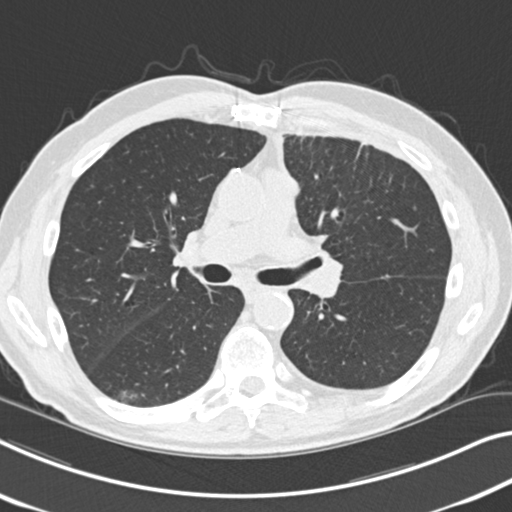
Axial slice from a low-dose chest CT screening exam, first (baseline) screen, lung window (W 1500 / L -600 HU), 2 mm slice thickness, 512 × 512 image matrix, field of view 338 × 338 mm. Male, age 68 years at enrolment. Current smoker at enrolment.
Expert reader's lesion annotation, bounding box <99,379,150,413> (left, top, right, bottom; pixels). The exam's reader record, not a measurement of the box and not confirmed to be the same lesion: non-calcified nodule or mass ≥4 mm, right lower lobe, 14 × 10 mm, poorly defined margins, ground glass attenuation. Official screen result: positive, change unspecified: nodule(s) >= 4 mm or enlarging nodule(s), mass(es), or other non-specific abnormalities suspicious for lung cancer.